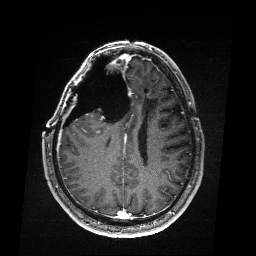
Brain MRI from a brain-tumour surgery series, one axial slice; slice 74 of 176 in the series (ordered by position); T1-weighted post-contrast; 256 × 256 image matrix, field of view 256 × 256 mm. Case-level facts recorded for this patient, not image findings: histopathology: Astrocytoma; WHO grade: 4.
Structures marked on this image (expert manual segmentation):
- residual tumour: bounding box [x1, y1, x2, y2] px = [99, 129, 105, 132]